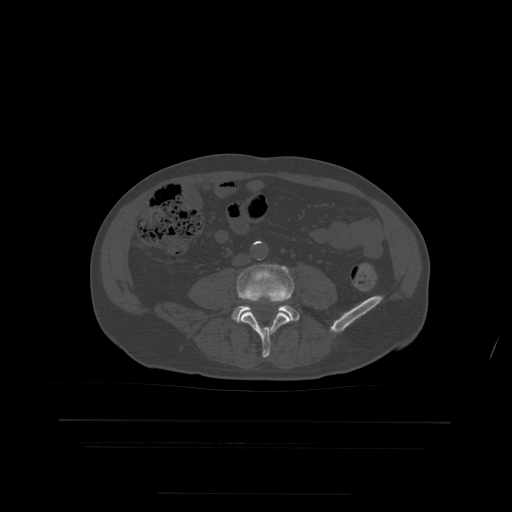
CT including the spine, one axial slice. Position 88 of 522 along the scan axis. Bone window (W 1800 / L 400 HU). 512 × 512 image matrix, field of view 436 × 436 mm. Patient age 68 years. From the clinical record (not read from this slice): primary cancer: urothelial.
Annotated regions visible in this slice (semi-automatic segmentation, software-assisted and operator-edited):
- L4 vertebra: bounding box <237,264,294,358> (left, top, right, bottom; pixels)
- L5 vertebra: <233,306,300,322>